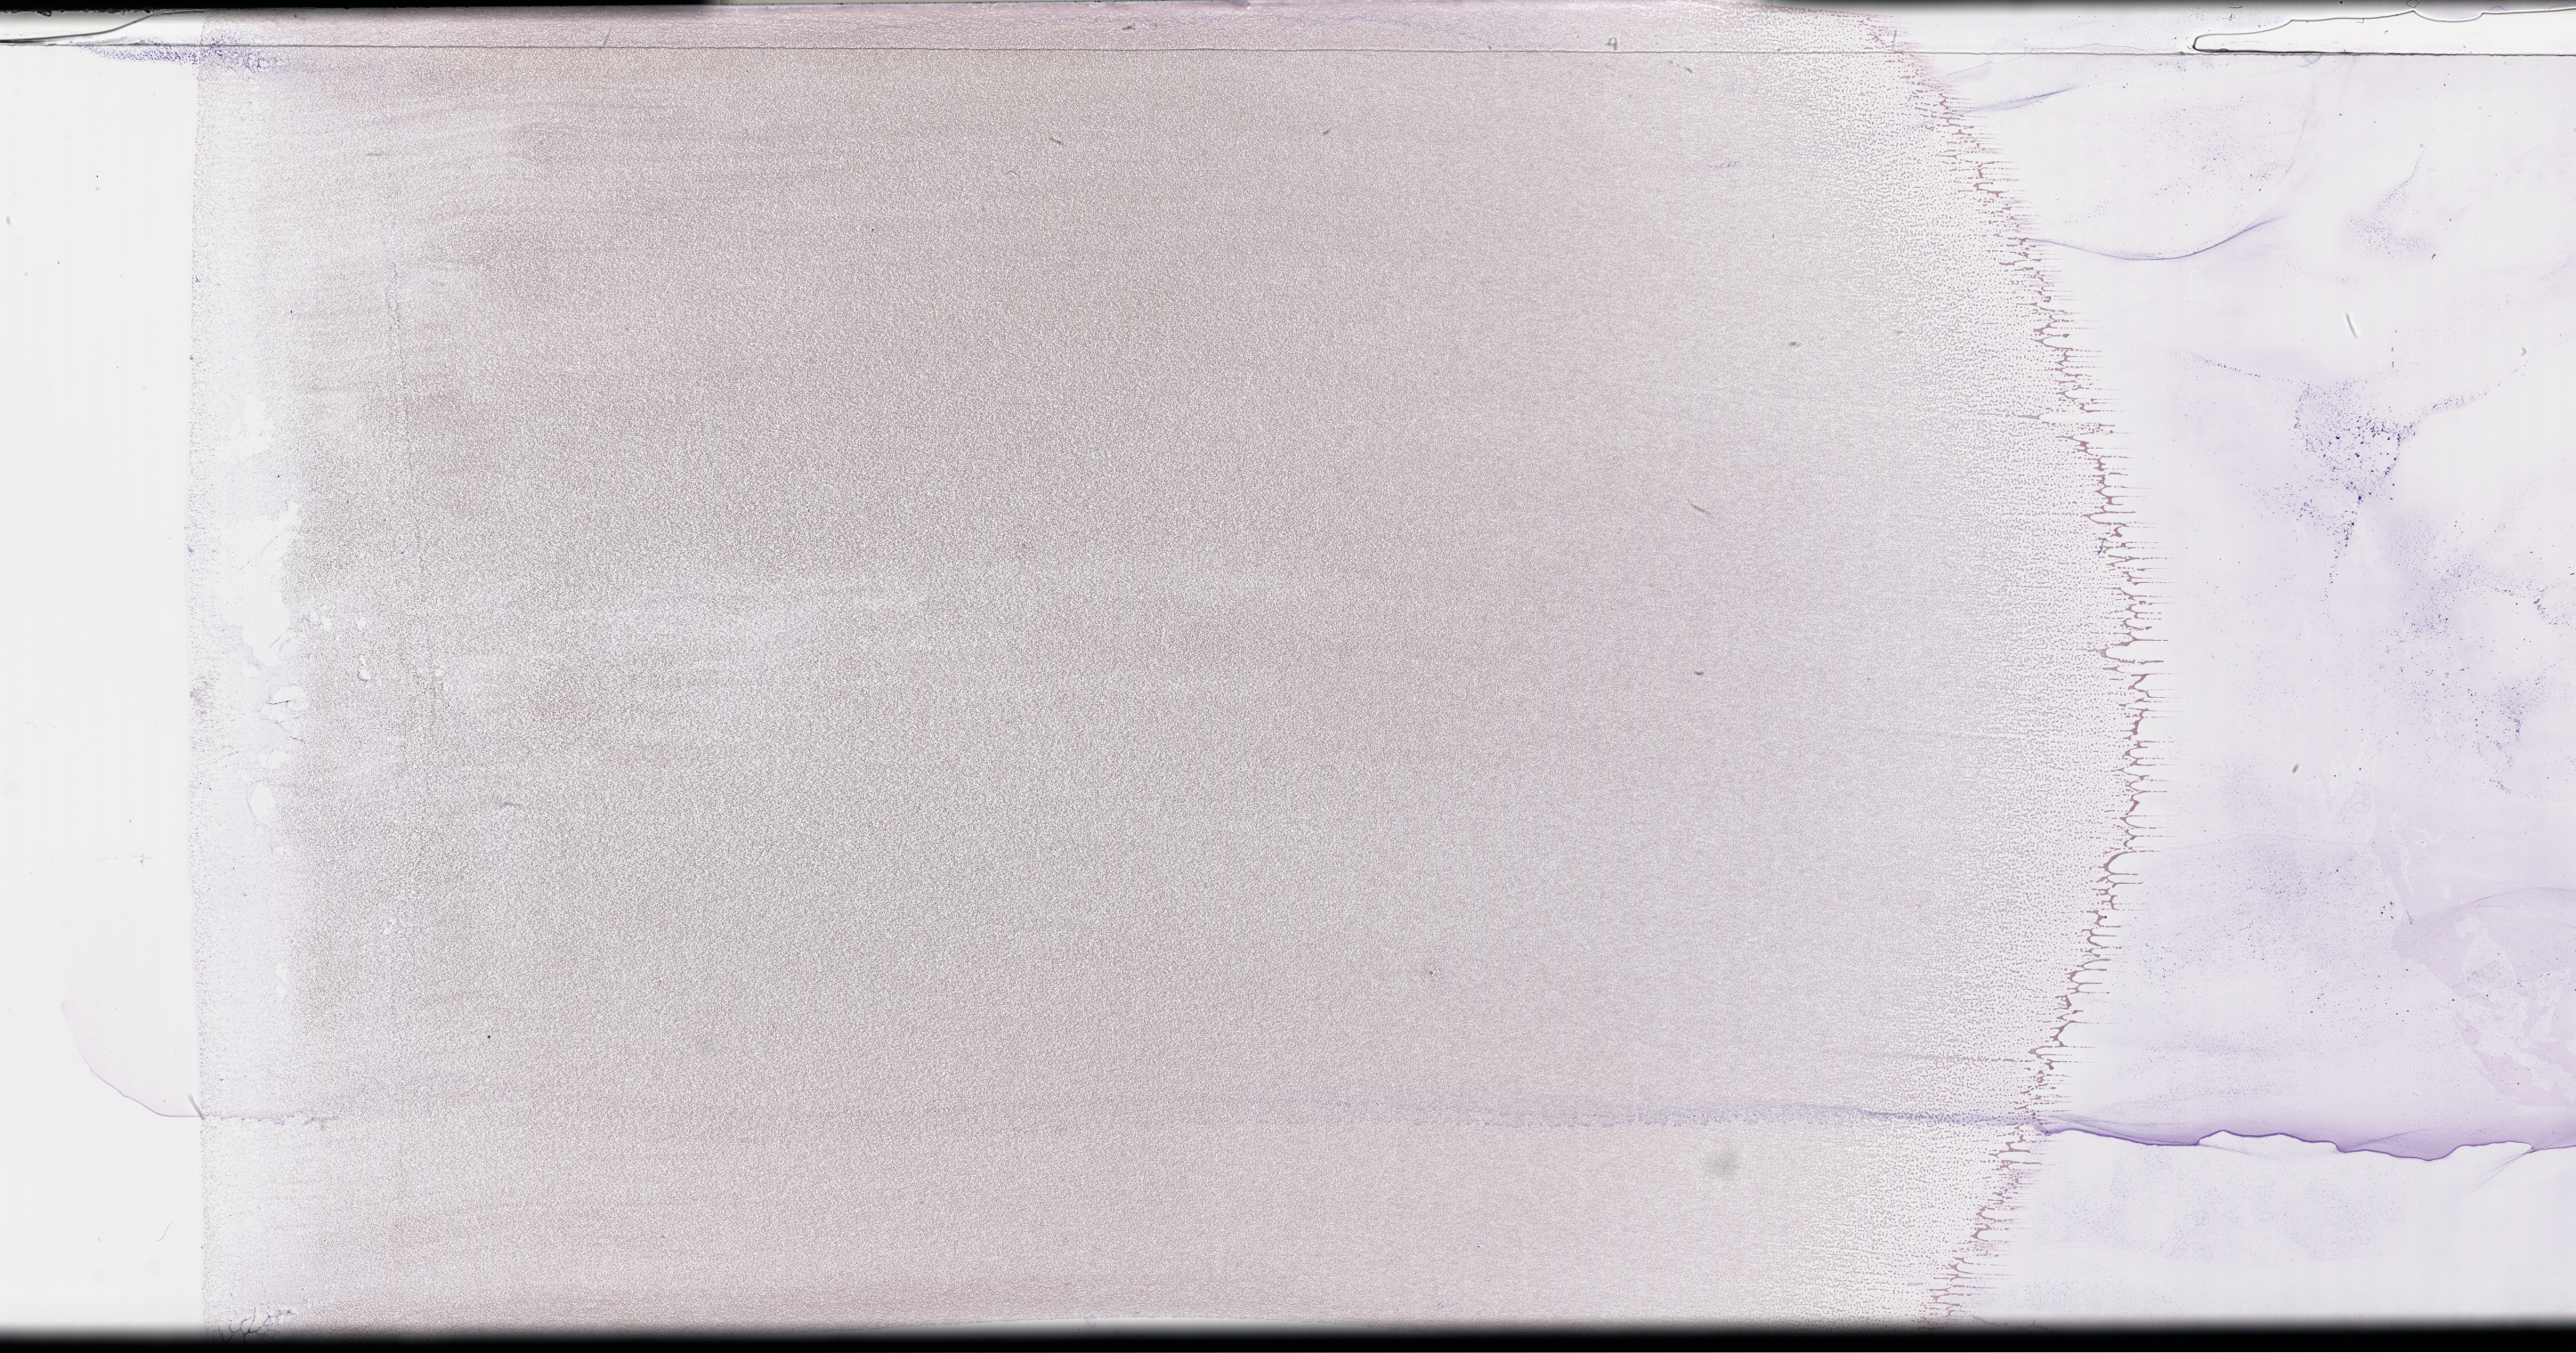
Whole-slide image of a whole blood smear, Wright-Giemsa stain — a low-resolution overview of the entire scanned area, about 46.7 x 24.5 mm; smear from an EDTA sample; collected on treatment. Patient sex: male.
Patient diagnosis: Acute Myeloid Leukemia Not Otherwise Specified.